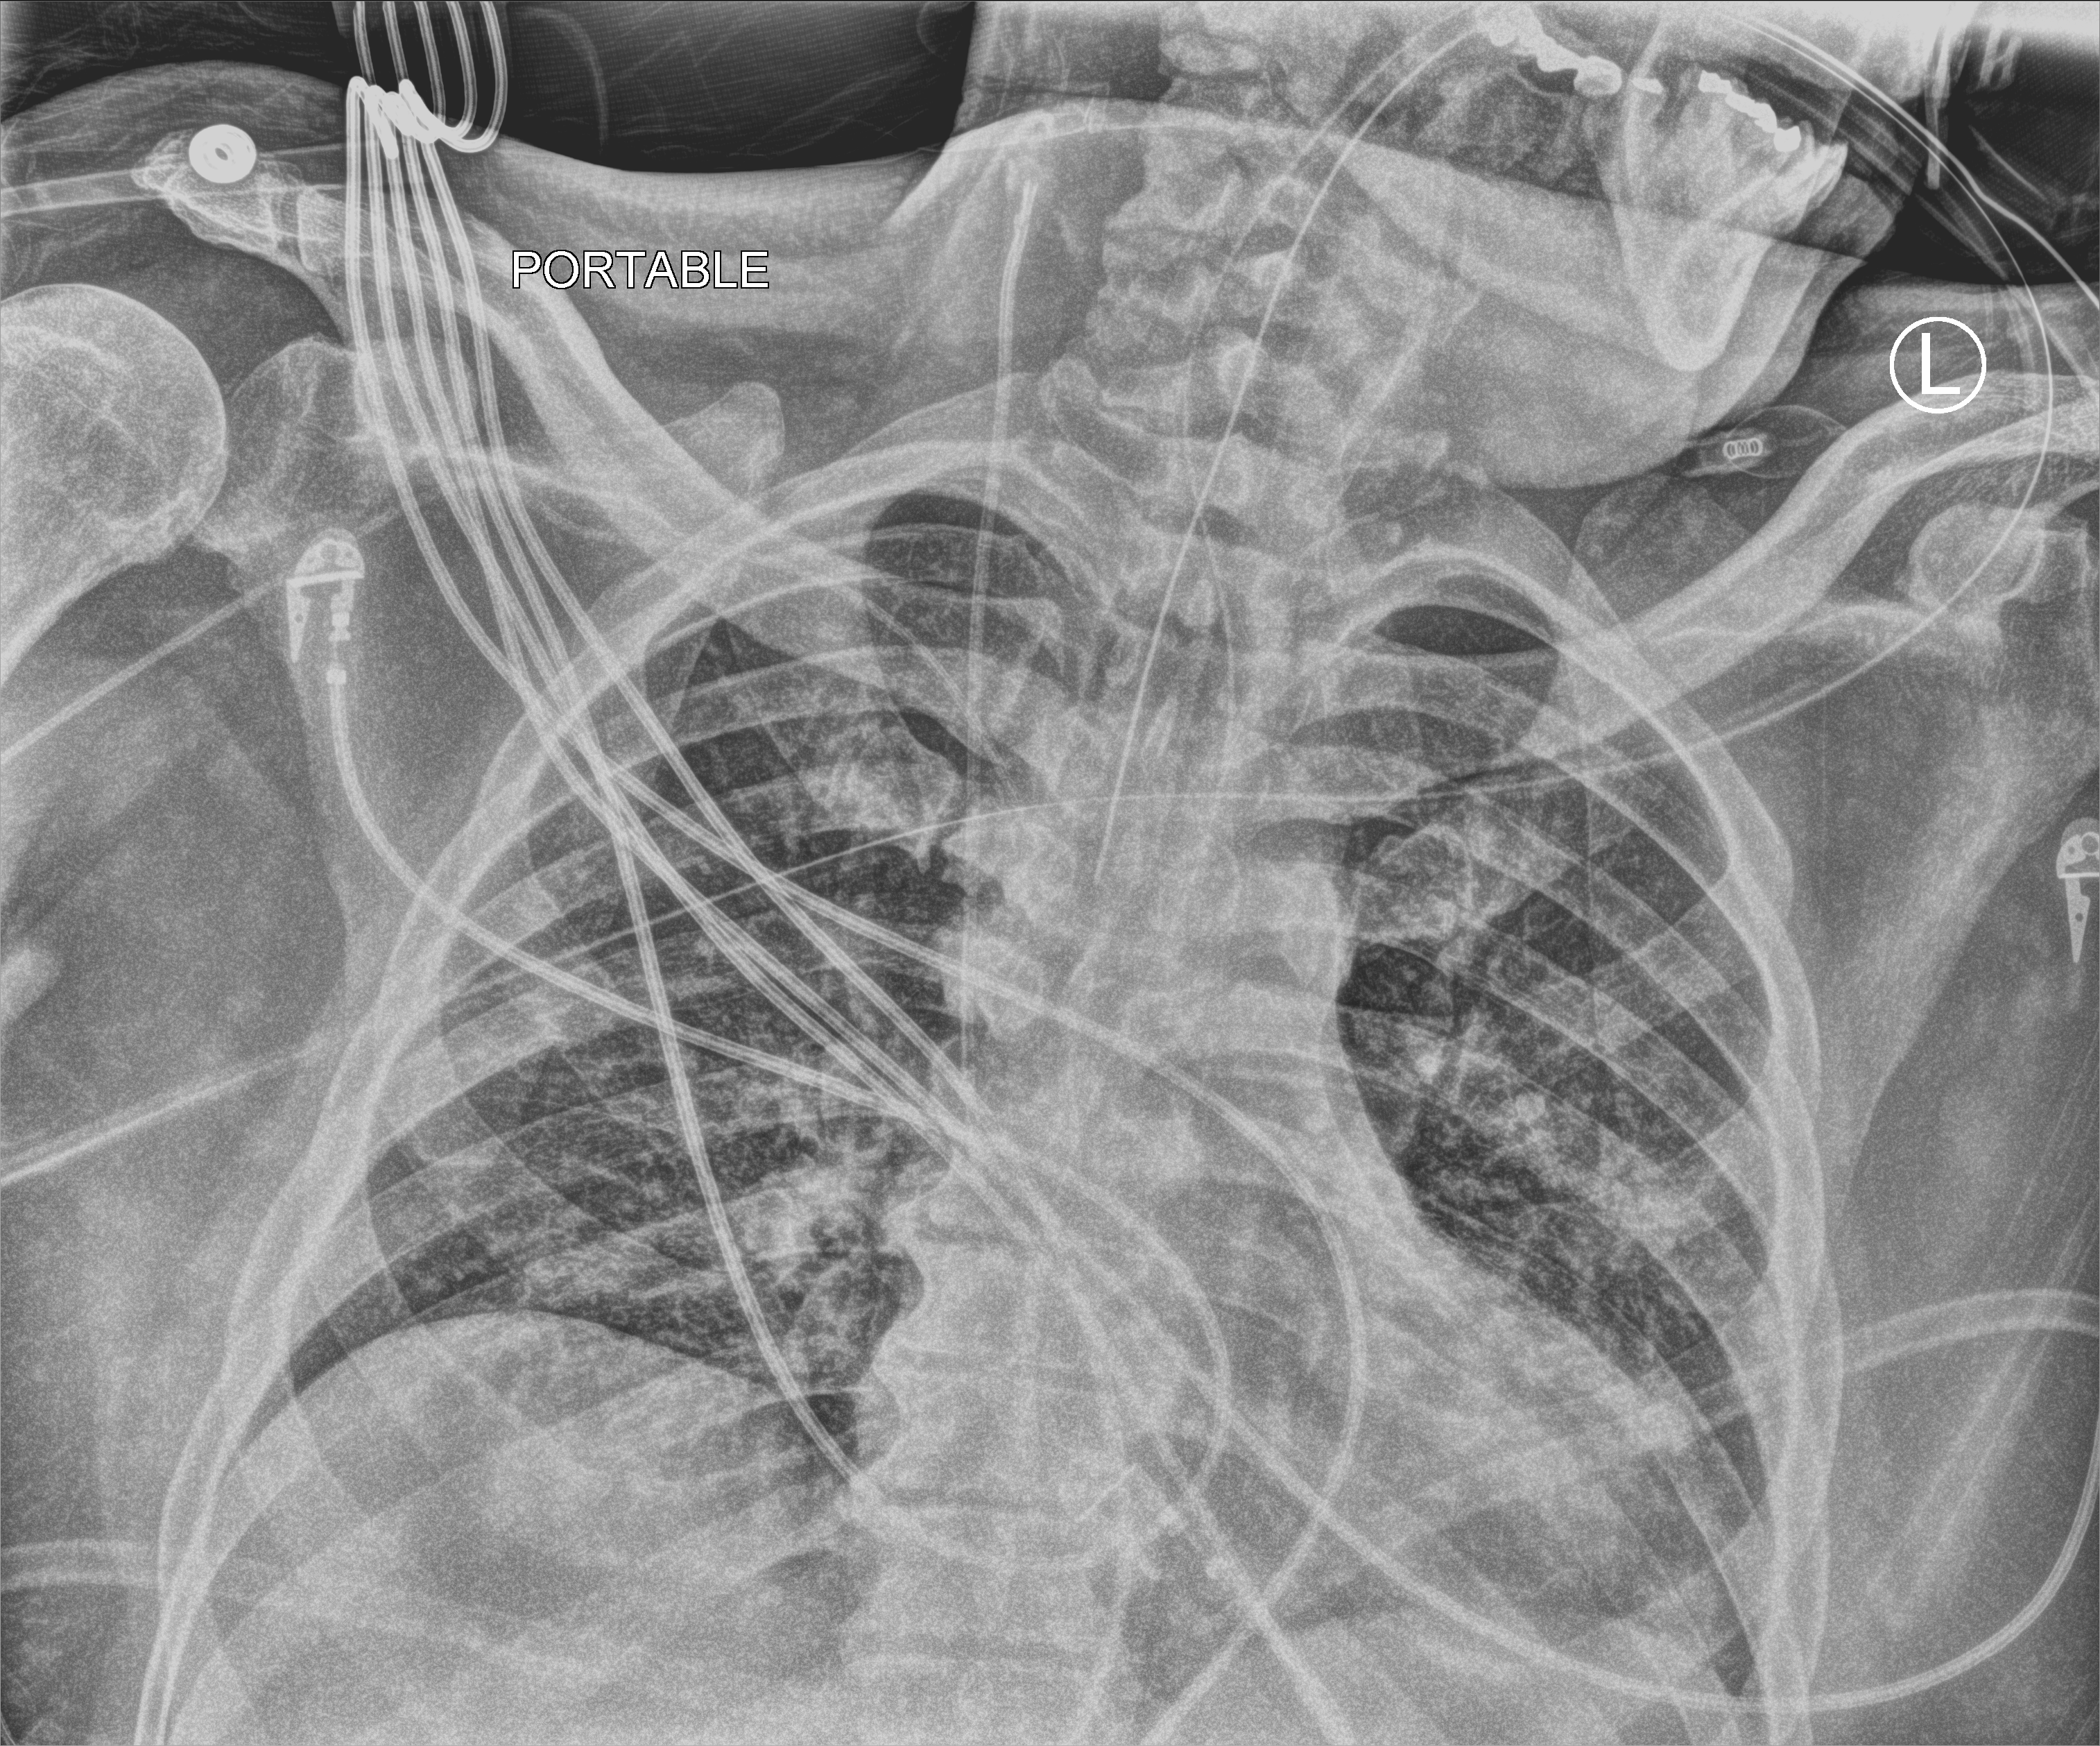
Chest X-ray (portable); anteroposterior (AP) projection. Patient hospitalised with COVID-19; male, aged 18–59 years.
Admission-level facts for this patient (not findings on this image; timing relative to this image not recorded):
- mechanically ventilated during this hospital stay: yes